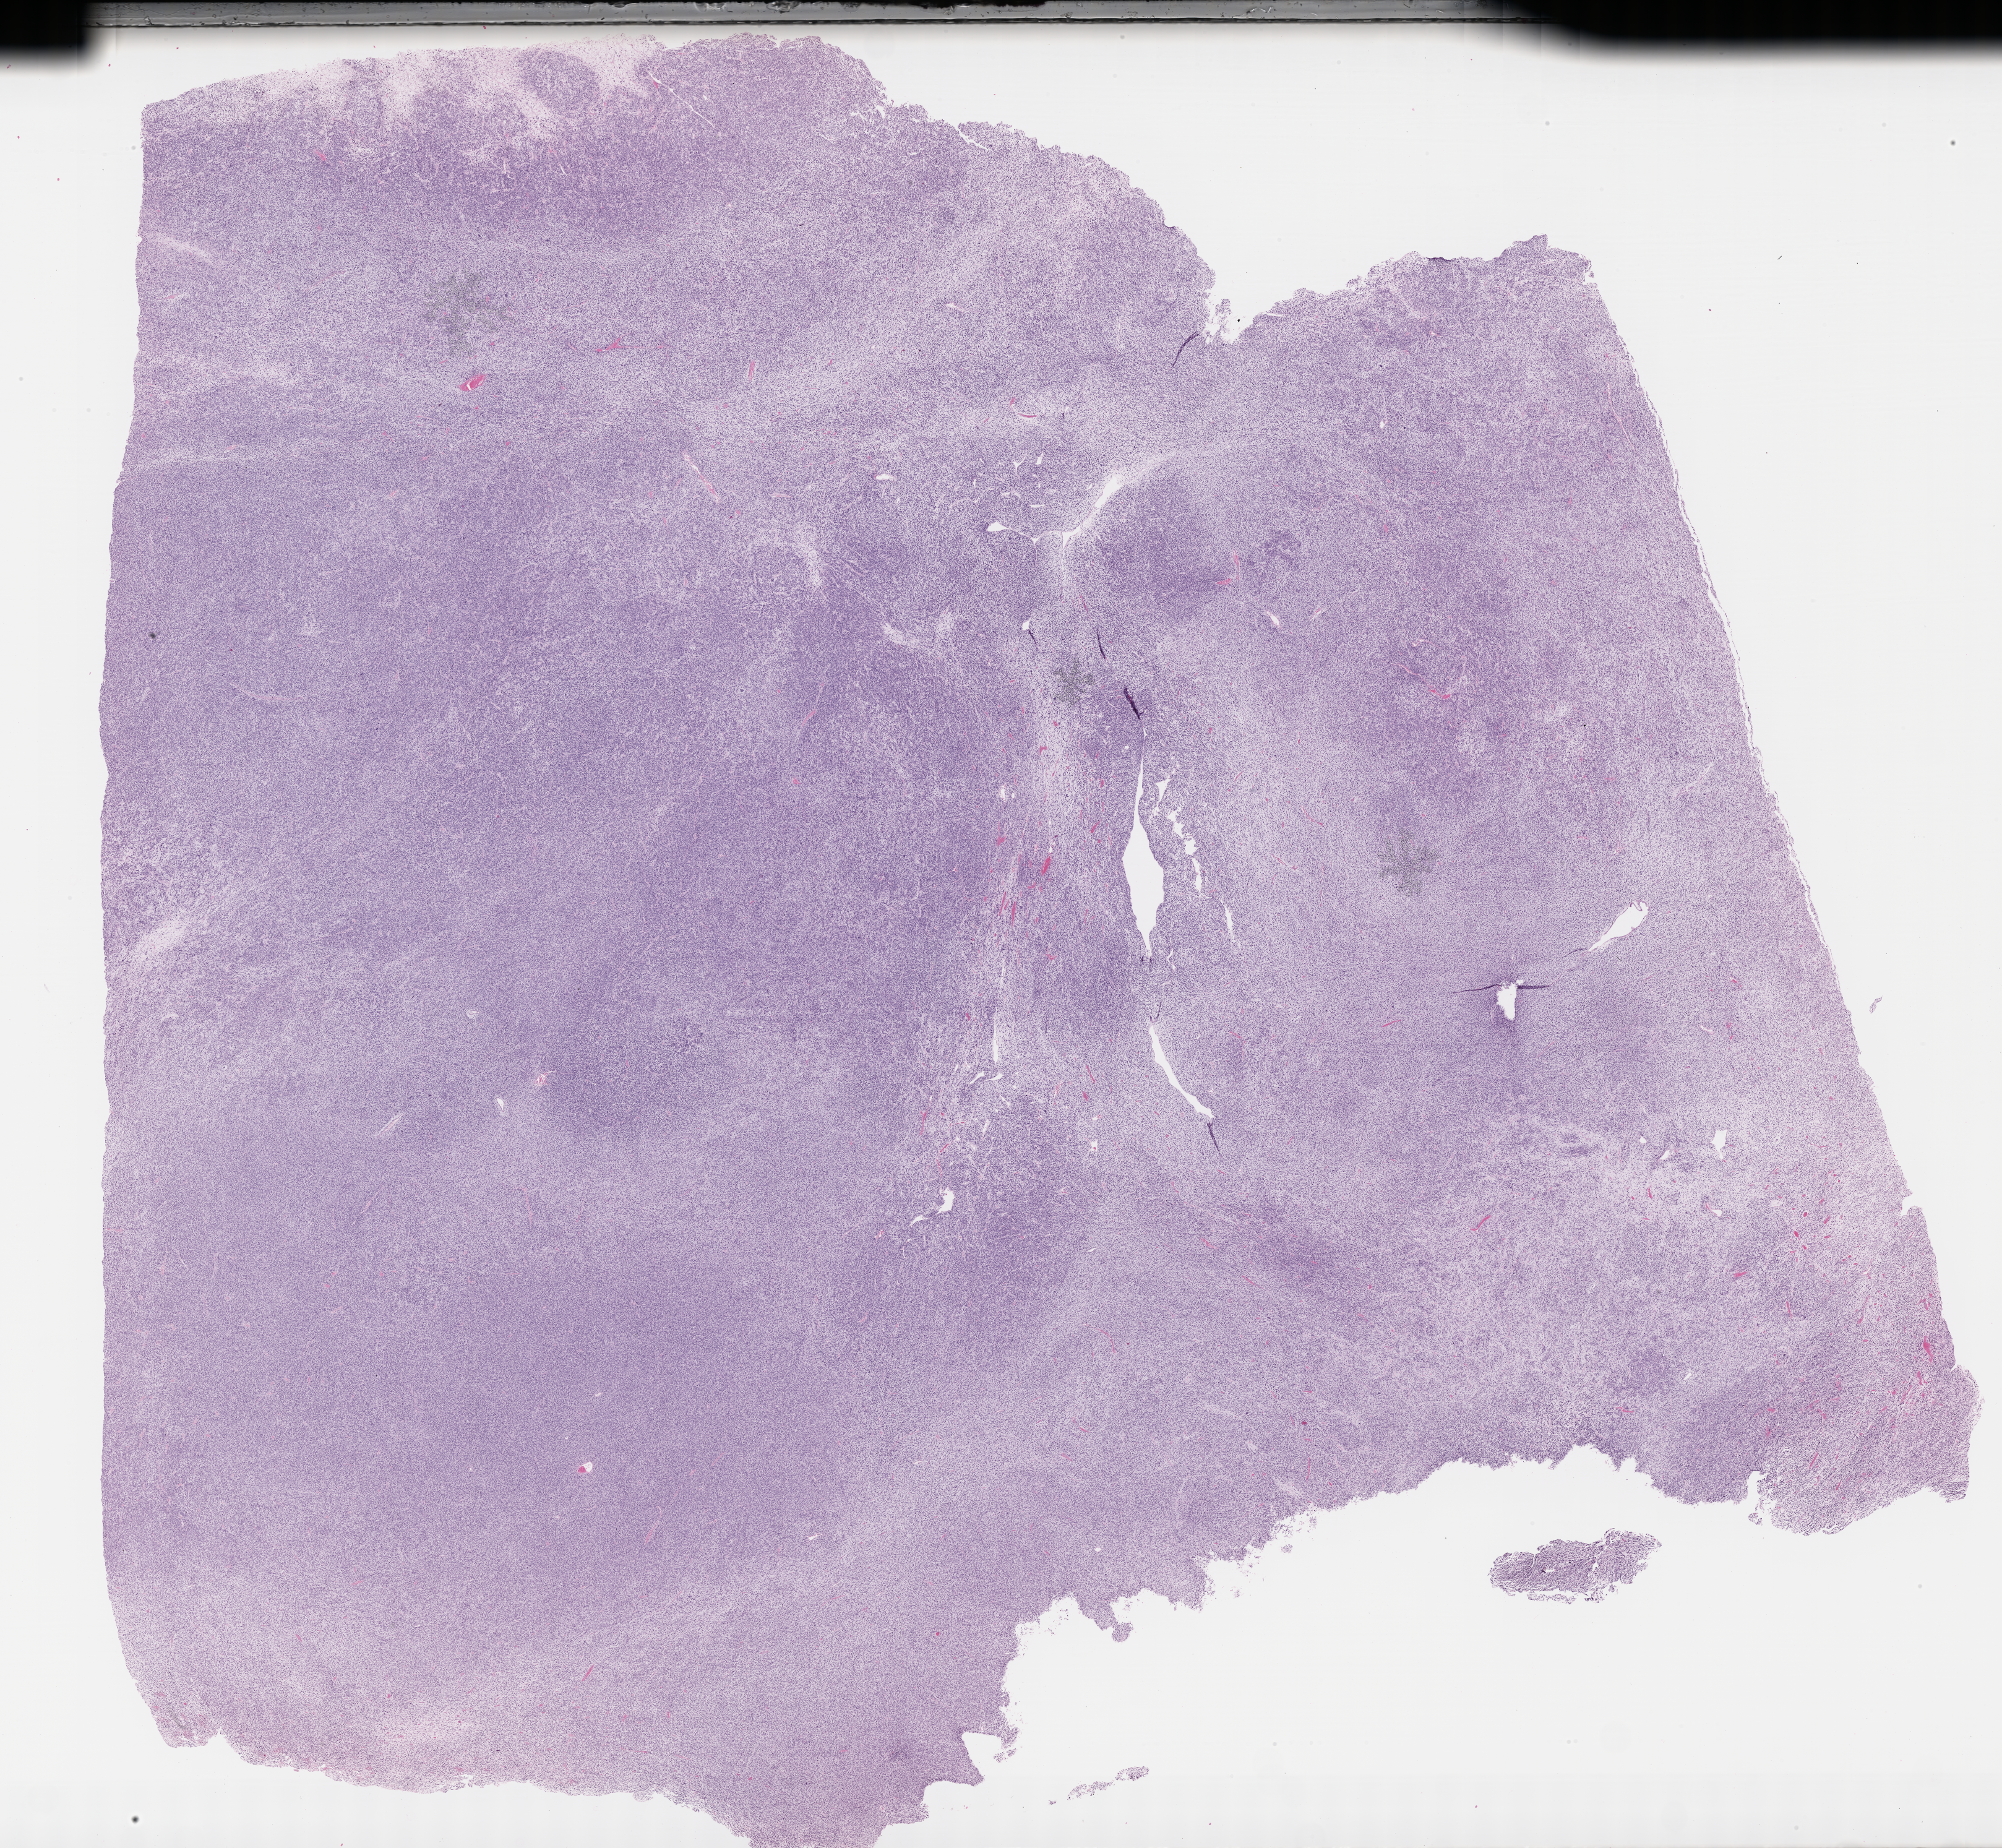
Haematoxylin and eosin whole-slide image of tumor tissue, whole scanned area (about 26.2 x 24.2 mm) shown as a low-resolution overview. Formalin-fixed paraffin-embedded section. Sample anatomic site: testicle-left. Patient: male, age 14.5 years at diagnosis.
• stage (as recorded): 1
• diagnosis: rhabdomyosarcoma; histological classification: embryonal rhabdomyosarcoma